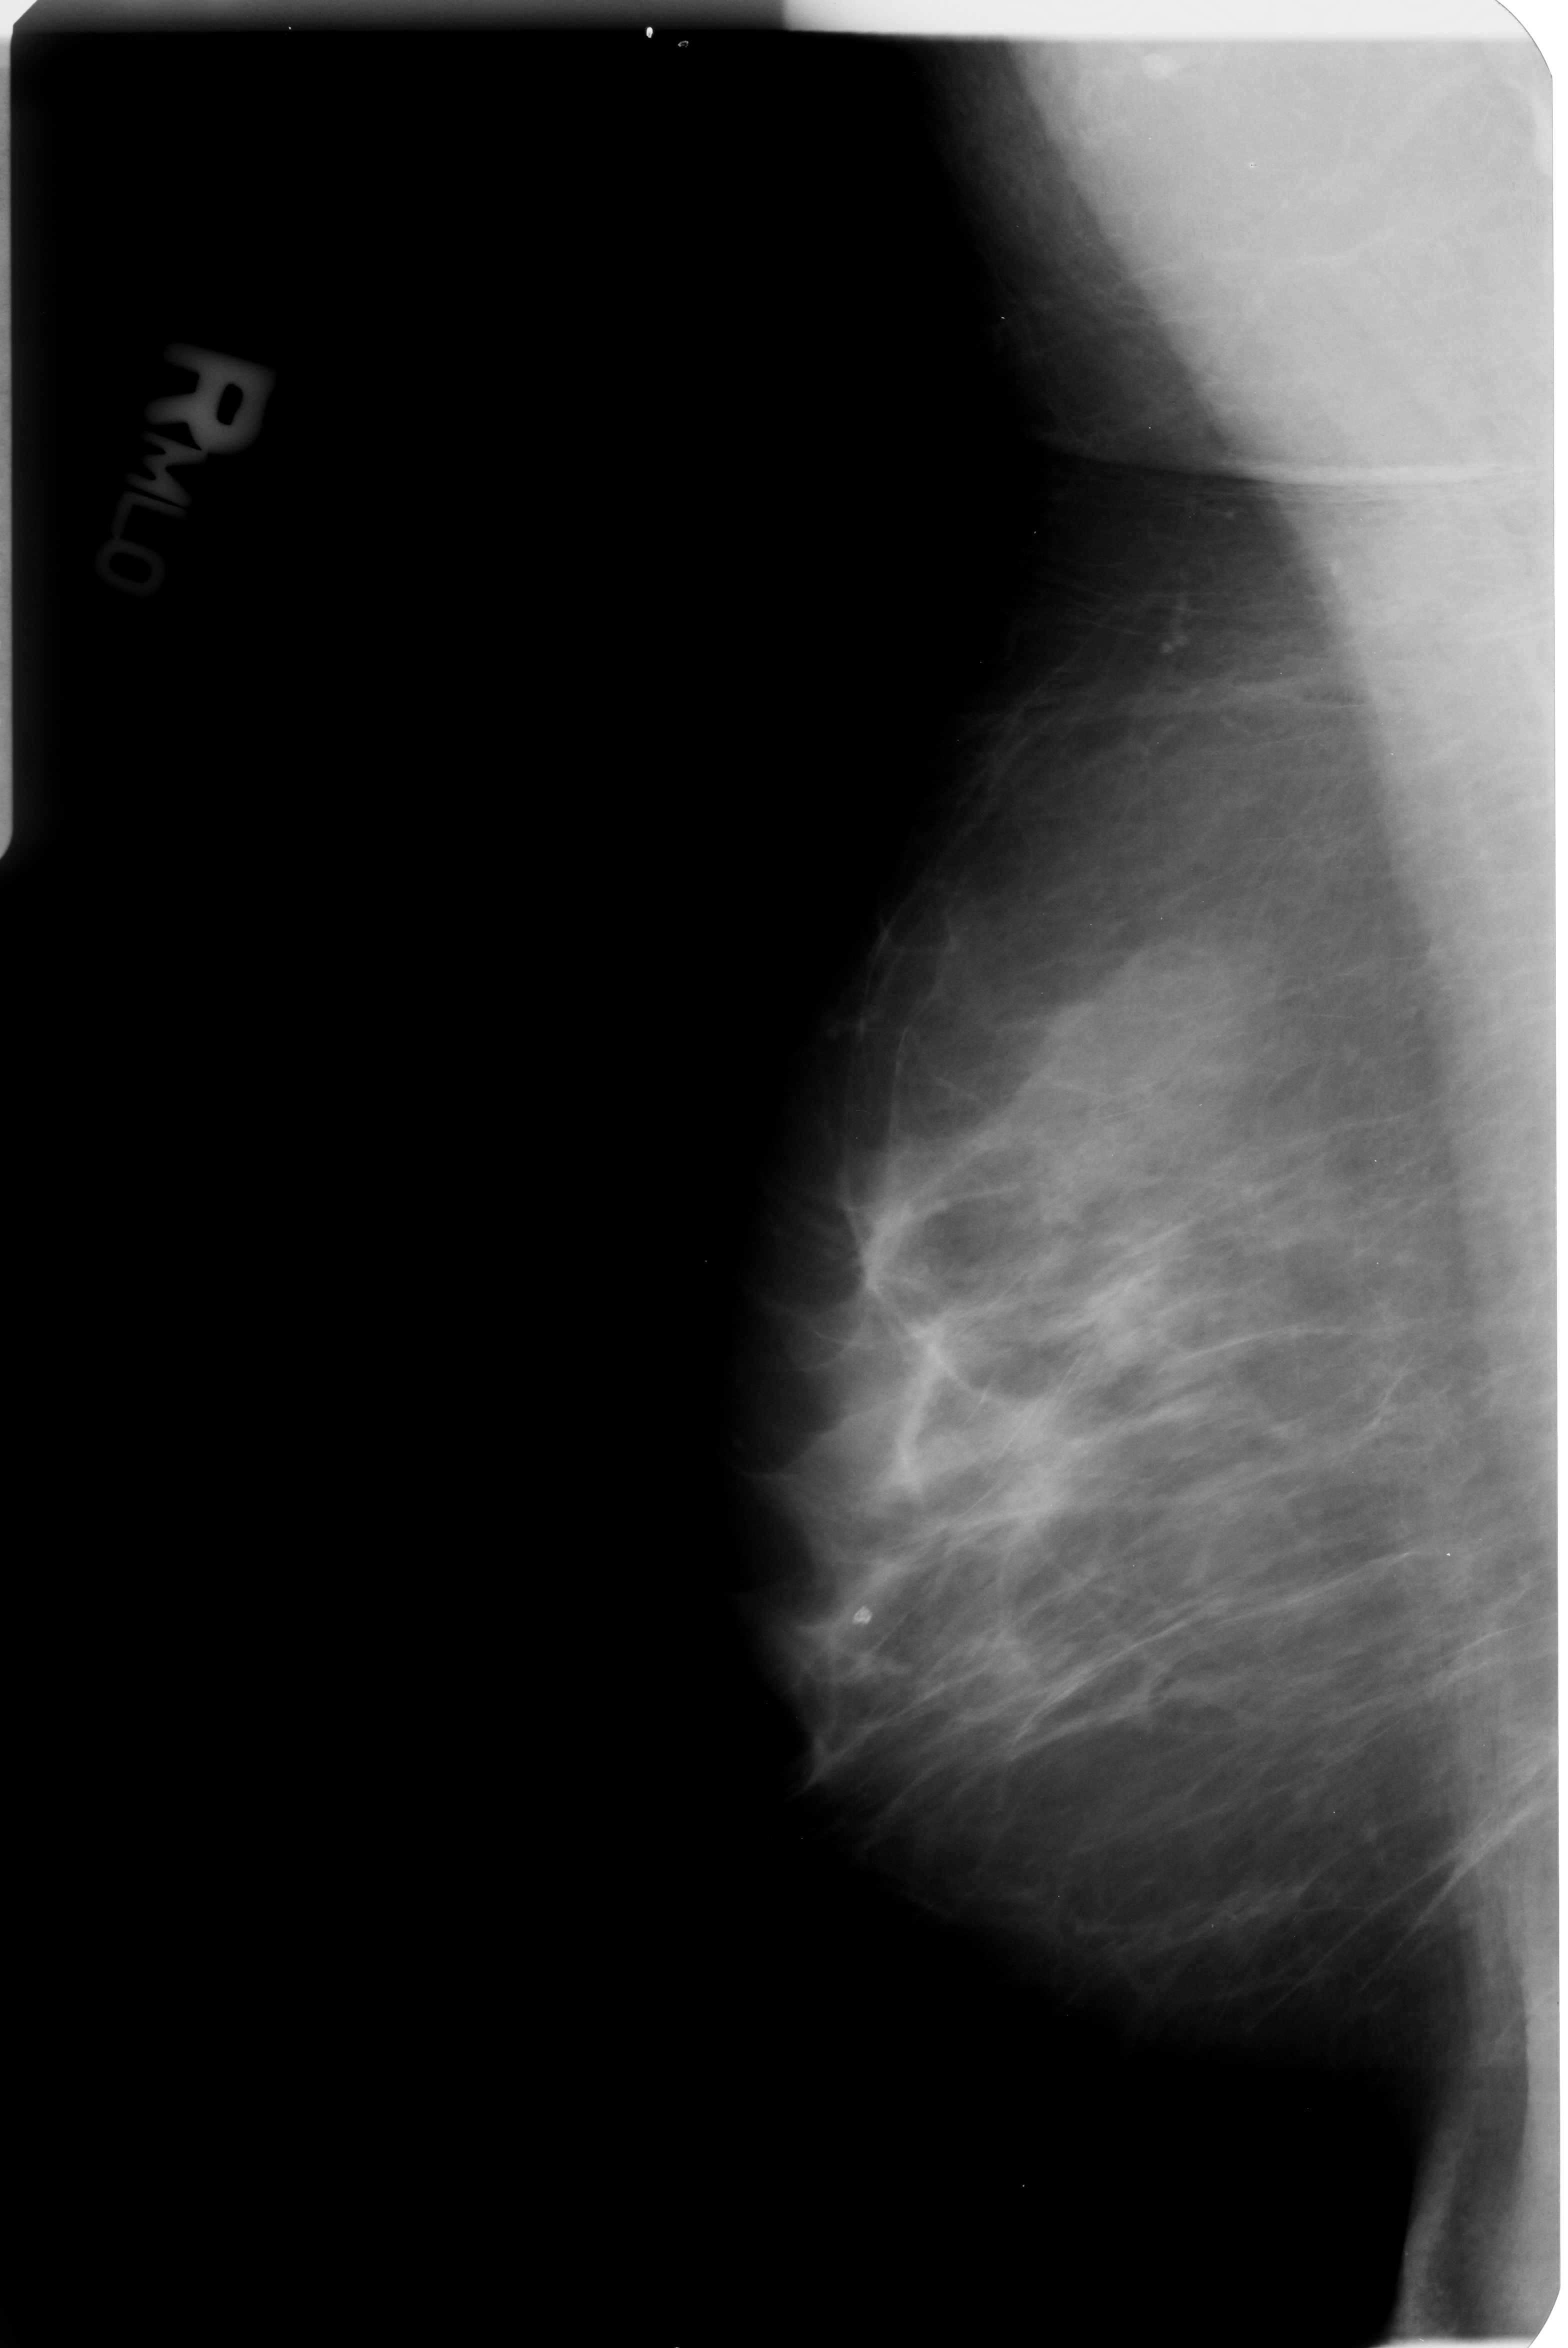
Scanned film-screen mammogram; right breast; MLO view; breast composition: scattered fibroglandular densities (BI-RADS density category 2 of 4); 1568 × 2348 image matrix.
Marked abnormalities (boxes around the expert regions of interest):
- calcifications, morphology lucent center; BI-RADS assessment category 2; subtlety rating 5 on a 1 (subtle) to 5 (obvious) scale; outcome (as recorded, no biopsy): benign without callback (not worked up further): bounding box <840,1600,881,1633> (left, top, right, bottom; pixels)